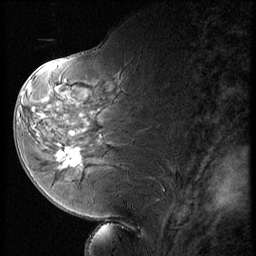
Breast MRI (dynamic contrast-enhanced), one sagittal slice. Position 29 of 56 along the scan axis. 3 images stored at this slice position (order not interpretable as contrast timing). 1.5 T. TE 4.2 ms, TR 9 ms. 2.5 mm slice thickness. 256 × 256 image matrix, field of view 180 × 180 mm. Patient: female, 58 years. Case-level facts recorded for this patient, not image findings: setting: breast cancer imaged before/during neoadjuvant chemotherapy; receptor status: HR-positive, HER2-negative.
Structures marked on this image (semi-automatically segmented with operator editing):
- analysis volume of interest (the breast-tissue region the enhancement analysis was run in; not a lesion): bounding box (x1, y1, x2, y2) in pixels: (47, 136, 88, 178)
- tumour enhancement mask (voxels above the 140 % enhancement threshold inside the analysis volume of interest): (57, 149, 82, 168)